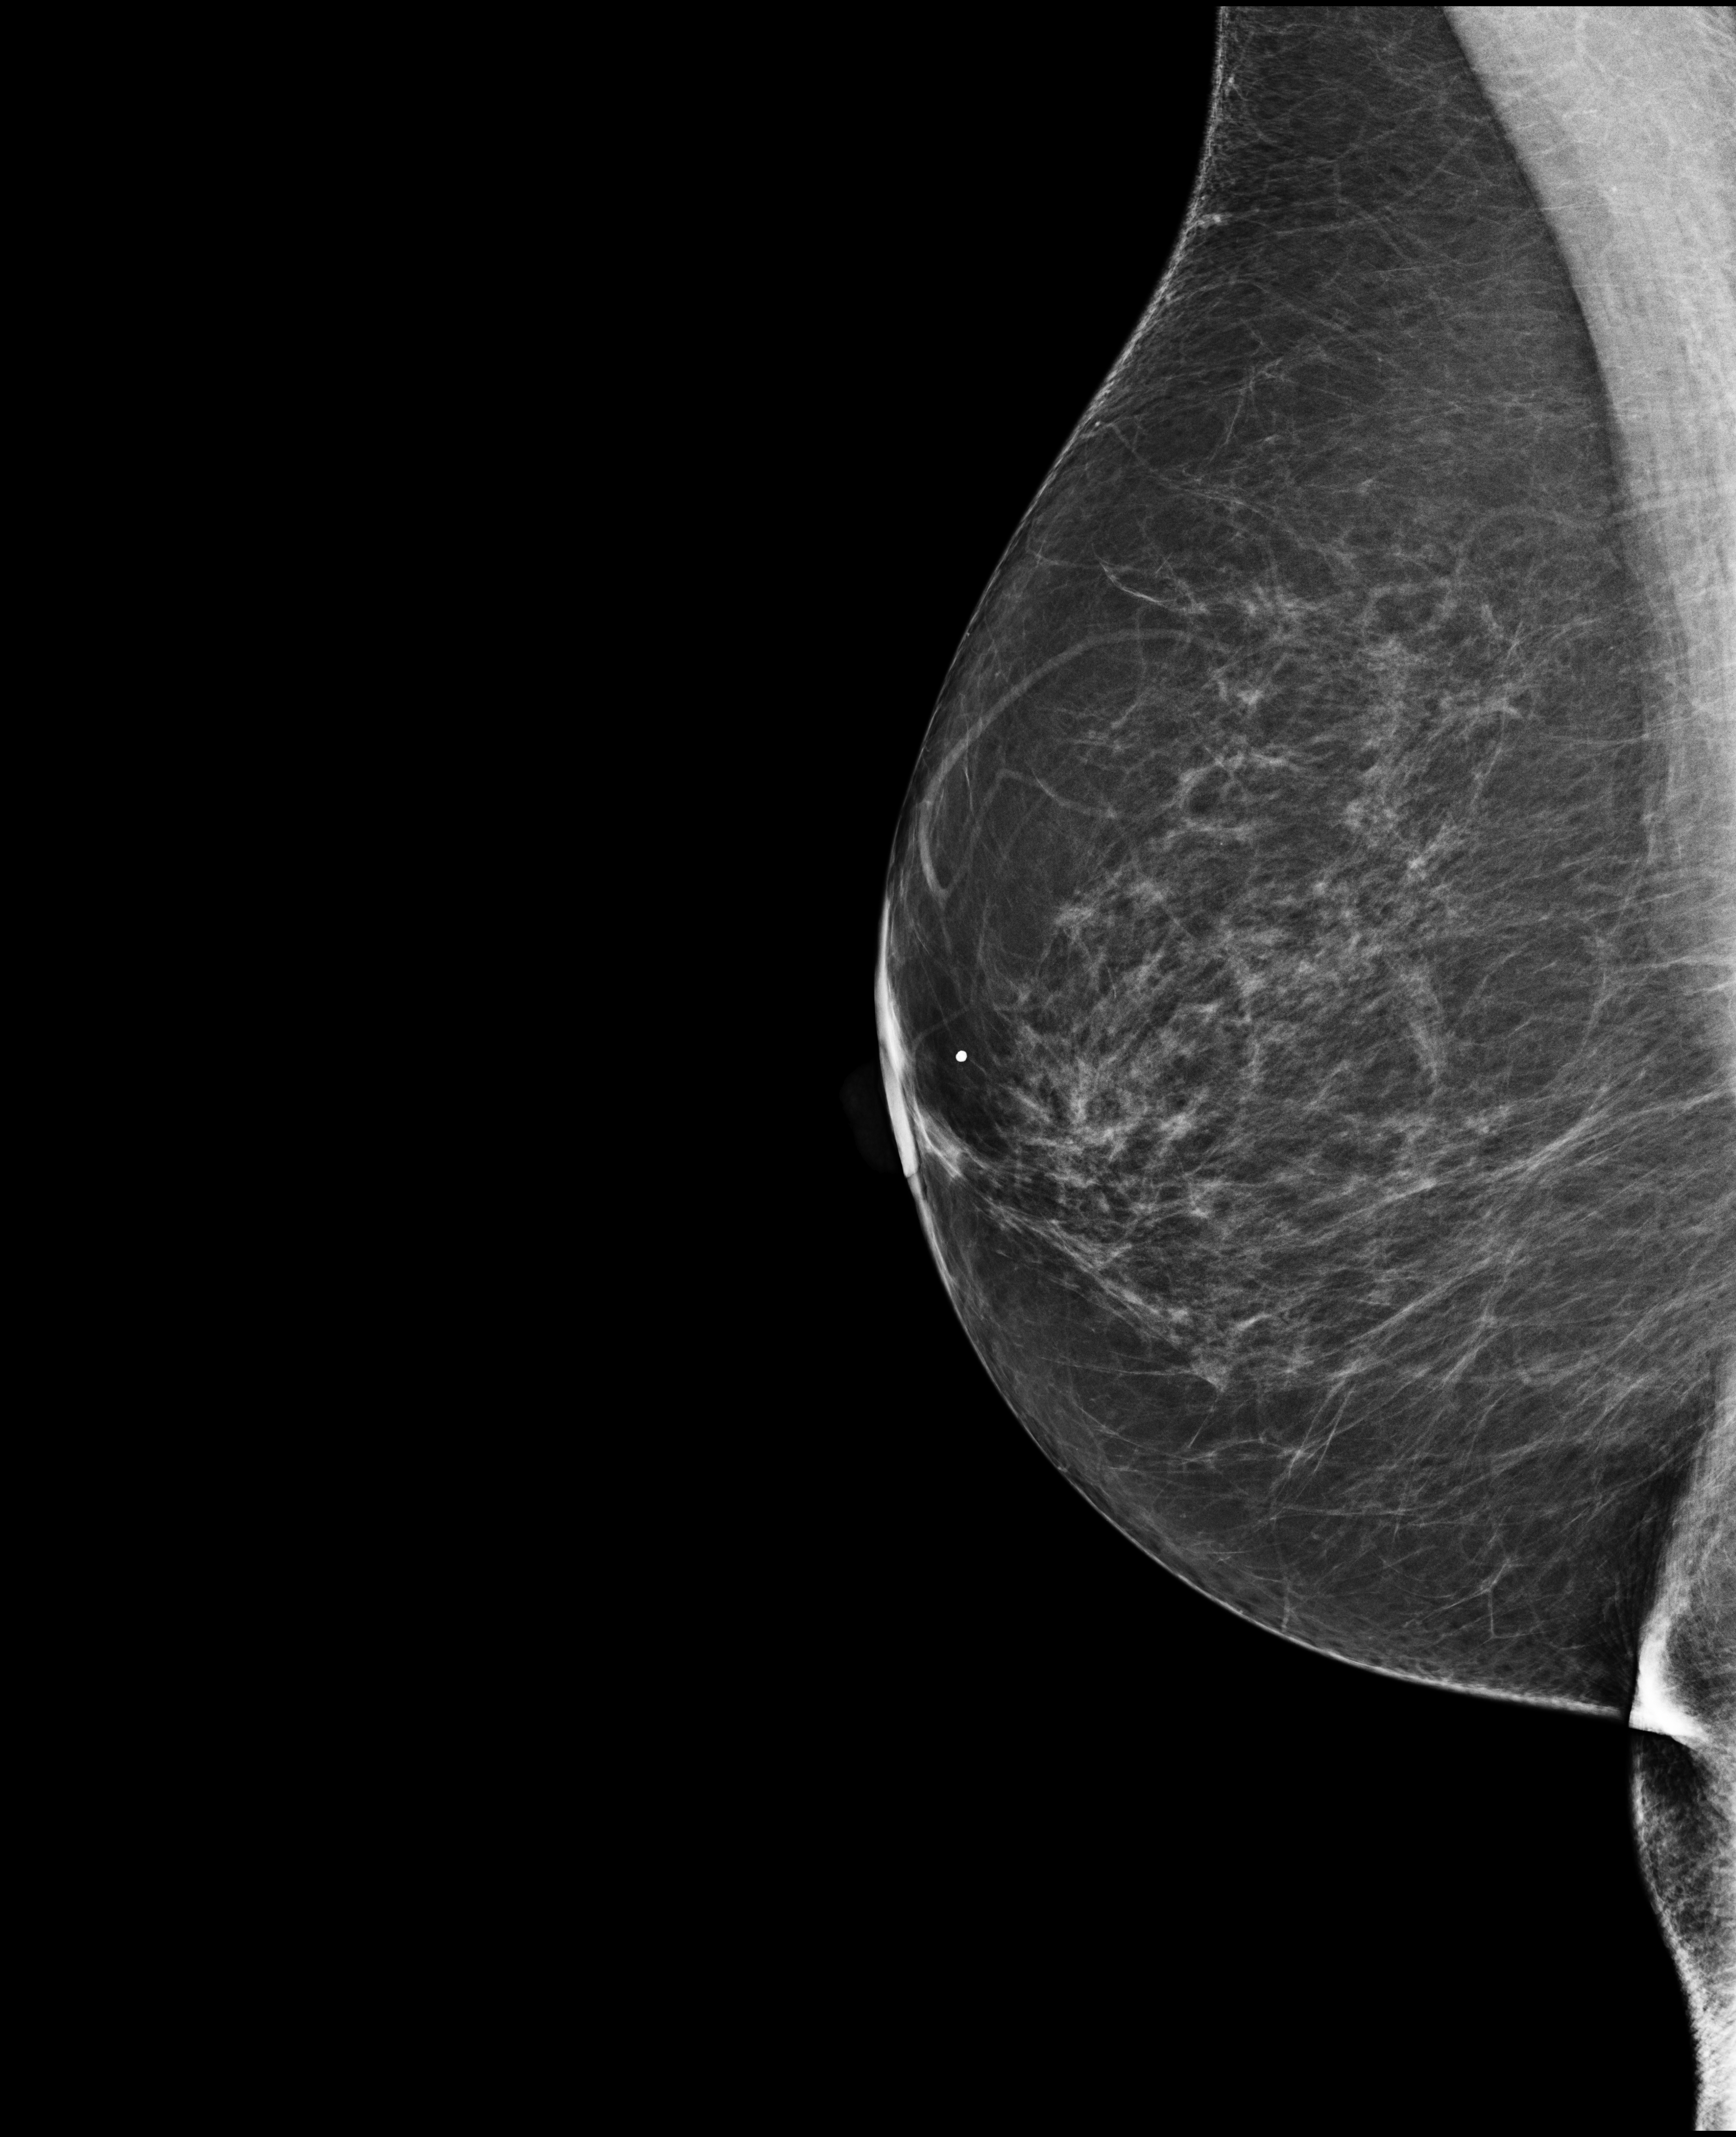
Digital mammogram (FFDM), right breast, medio-lateral oblique projection, annual screening mammography examination, compressed breast thickness 80 mm, system: Selenia Dimensions. Female patient, age 74 years.
Breast density at the screening exam (both breasts): heterogeneously dense (BI-RADS density category c). Final BI-RADS category for the screening round (tomosynthesis exam, both breasts): category 4. Recall: recalled for additional imaging after this screen.